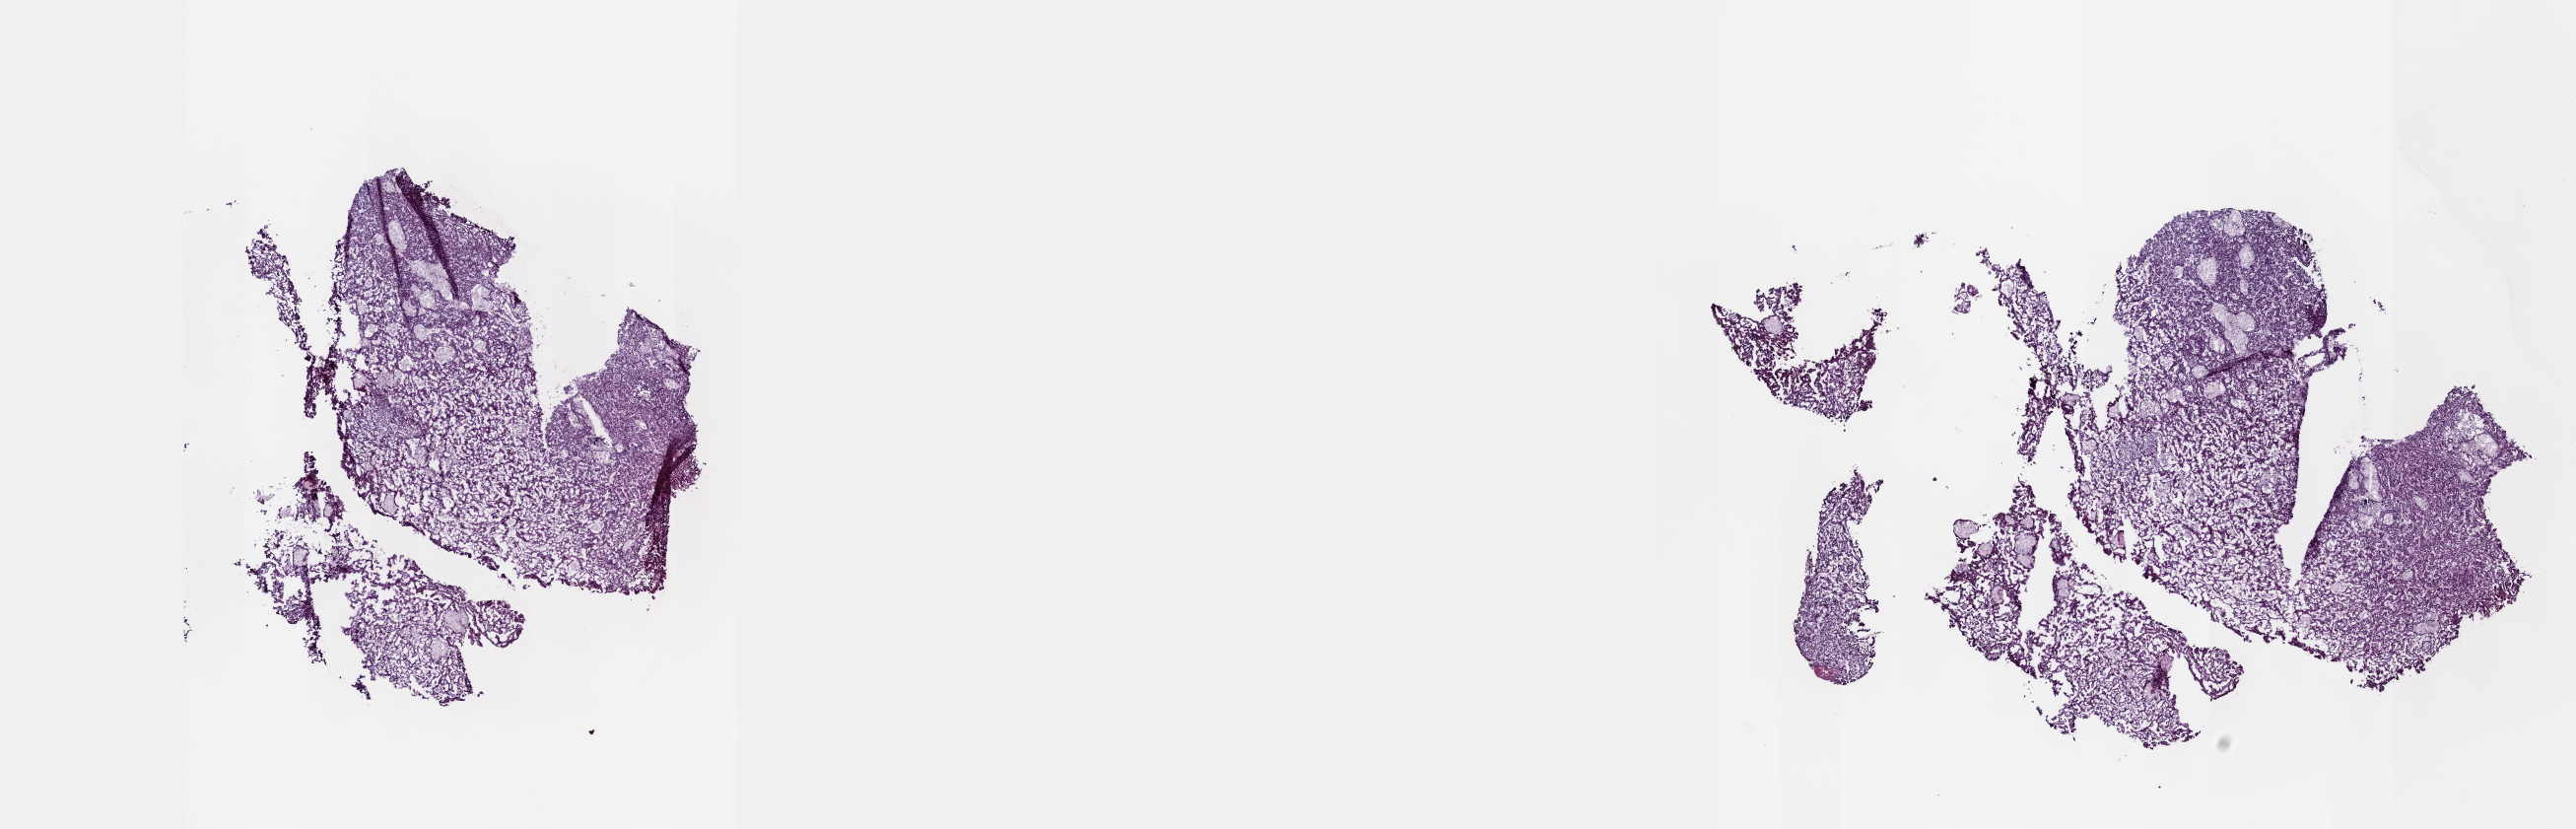
H&E-stained whole-slide image — low-resolution overview of the scanned area, about 21.1 x 6.8 mm. Frozen section from the top of the tissue portion. Primary tumour sample from the kidney. Male, age 73 years at initial diagnosis. Slide review estimates, as recorded: tumour cells 100%, tumour nuclei 94%, normal cells 0%, stromal cells 0%, necrosis 0%. Inflammatory infiltration, as recorded: lymphocyte infiltration 0%, monocyte infiltration 0%, neutrophil infiltration 0%.
TNM: T1 N0 MX. Histologic diagnosis: Papillary adenocarcinoma, NOS. AJCC pathologic stage: I (6th edition). Laterality: right.